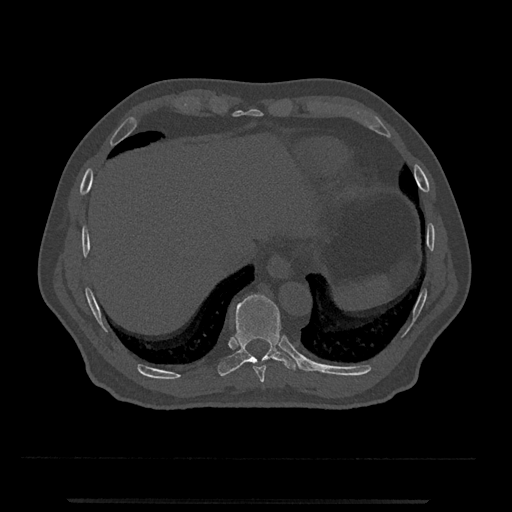
CT including the spine, one axial slice; slice 535 of 797 in the series (ordered by position); reconstruction kernel Br40s/3; bone window (W 1800 / L 400 HU); 0.5 mm slice thickness; 512 × 512 image matrix. Patient: male, 63 years. From the clinical record (not read from this slice): primary cancer: prostate.
Structures marked on this image (semi-automatic segmentation, software-assisted and operator-edited):
- T10 vertebra: bounding box <218,294,299,376> (left, top, right, bottom; pixels)
- T9 vertebra: <253,365,266,383>